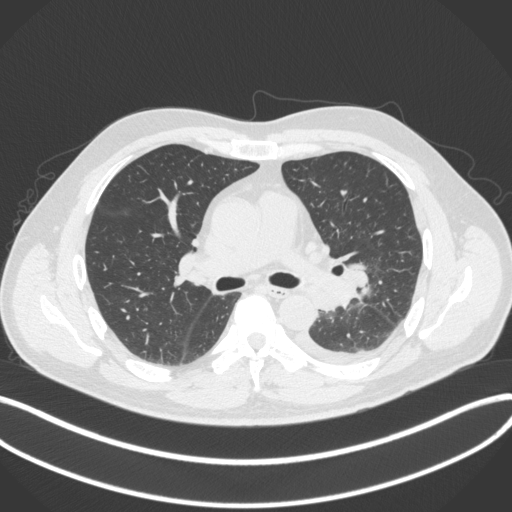
Chest CT, one axial slice. Slice 217 of 350 in the series (ordered by position). 120 kVp. Lung window (W 1500 / L -600 HU). 1 mm slice thickness. 512 × 512 image matrix, field of view 400 × 400 mm. Male patient, age 58 years. Case-level facts recorded for this patient, not image findings: clinical TNM (as recorded): T3 N1 M1b.
Structures marked on this image (rectangle marked by the reading radiologist):
- lung tumour (recorded histology: small cell carcinoma): bounding box <335,260,371,311> (left, top, right, bottom; pixels)